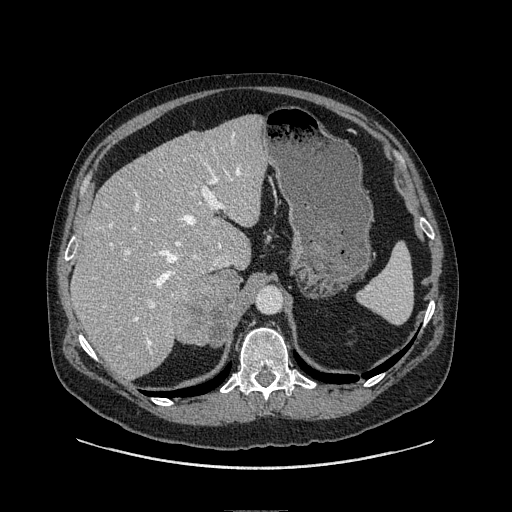
Contrast-enhanced abdominal CT, one axial slice; position 71 of 149 along the scan axis; soft-tissue window (W 400 / L 40 HU); 1.25 mm slice thickness; 512 × 512 image matrix, field of view 440 × 440 mm. Male patient. Case-level facts recorded for this patient, not image findings: diagnosis: adrenocortical carcinoma; tumour side: right adrenal.
Outlined on this slice (semi-automatically segmented with operator editing):
- mass: box from (x=173, y=267) to (x=238, y=347) px